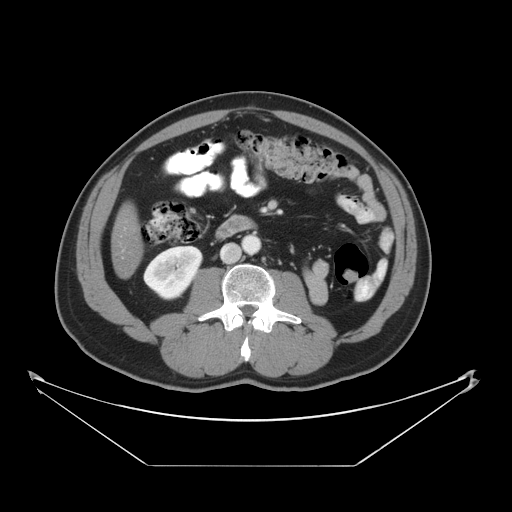
Contrast-enhanced abdominal CT, one axial slice. Position 11 of 46 along the scan axis. Reconstruction kernel STANDARD. 120 kVp. Intravenous contrast given. Soft-tissue window (W 400 / L 40 HU). 5 mm slice thickness. 512 × 512 image matrix. Male patient, age 57 years. Case-level facts recorded for this patient, not image findings: diagnosis: colorectal cancer liver metastases, imaged before liver resection; multiple liver metastases: no; largest metastasis: 3.3 cm; chemotherapy before resection: yes.
Annotated regions visible in this slice (expert manual segmentation):
- liver: bounding box <113,208,141,275> (left, top, right, bottom; pixels)
- planned liver remnant (the part of the liver to remain after resection): <113,207,141,275>